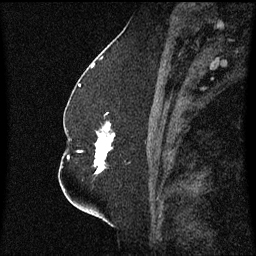
Breast MRI (dynamic contrast-enhanced), one sagittal slice; dynamic contrast-enhanced series, image 2 of 3 at this slice position (ordered by acquisition); 1.5 T; TE 4.2 ms, TR 8.4 ms; 256 × 256 image matrix, field of view 200 × 200 mm. Patient: female, 52 years. Case-level facts recorded for this patient, not image findings: setting: breast cancer imaged before/during neoadjuvant chemotherapy; receptor status: HR-positive, HER2-negative.
Structures marked on this image (semi-automatically segmented with operator editing):
- analysis volume of interest (the breast-tissue region the enhancement analysis was run in; not a lesion): bounding box [x1, y1, x2, y2] px = [94, 122, 128, 175]
- tumour enhancement mask (voxels above the 70 % enhancement threshold inside the analysis volume of interest): [94, 122, 114, 175]